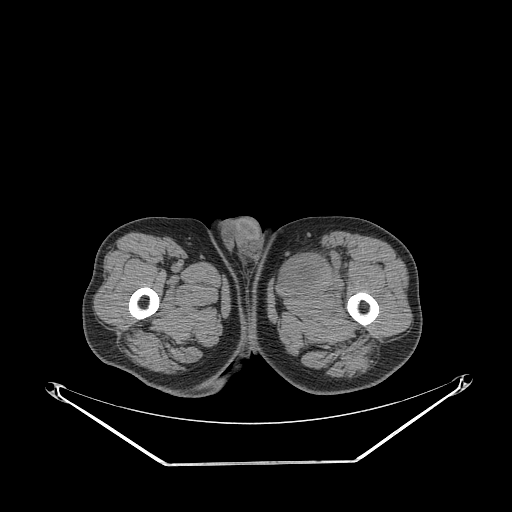
CT of an extremity soft-tissue mass (from a PET/CT study), one axial slice. Slice 264 of 267 in the series (ordered by position). Reconstruction kernel STANDARD. Soft-tissue window (W 400 / L 40 HU). 3.75 mm slice thickness. 512 × 512 image matrix. Male patient. From the clinical record (not read from this slice): histological type: pleiomorphic liposarcoma; grade: high; site of the primary tumour: left thigh.
Outlined on this slice (expert contour drawn on MRI and transferred to this co-registered scan by the dataset authors):
- gross tumour volume including surrounding oedema: box from (x=281, y=246) to (x=346, y=293) px
- gross tumour volume (mass): (x=281, y=251)–(x=325, y=284)